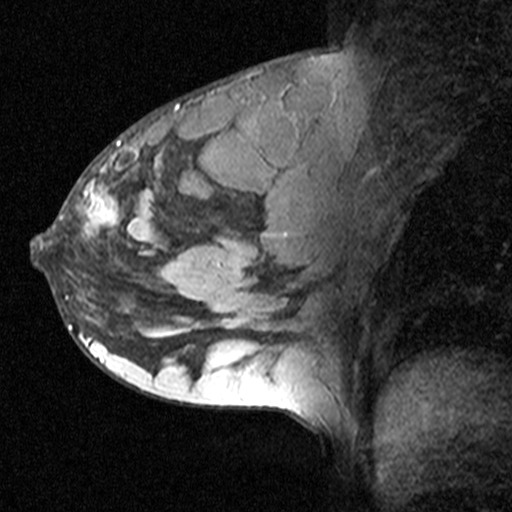
Breast MRI (dynamic contrast-enhanced), one sagittal slice. Dynamic contrast-enhanced study with each time point stored as its own series, time point 2 of 3 at this slice position (early post-contrast, ordered by acquisition time). 1.5 T. TE 4.5 ms, TR 11 ms. 3 mm slice thickness. 512 × 512 image matrix, field of view 200 × 200 mm. Female patient, age 27 years. Case-level facts recorded for this patient, not image findings: setting: breast cancer imaged before/during neoadjuvant chemotherapy; receptor status: HR-positive, HER2-negative.
Structures marked on this image (semi-automatic segmentation, software-assisted and operator-edited):
- analysis volume of interest (the breast-tissue region the enhancement analysis was run in; not a lesion): box from (x=36, y=162) to (x=163, y=271) px
- tumour enhancement mask (voxels above the 90 % enhancement threshold inside the analysis volume of interest): (x=60, y=168)–(x=133, y=240)